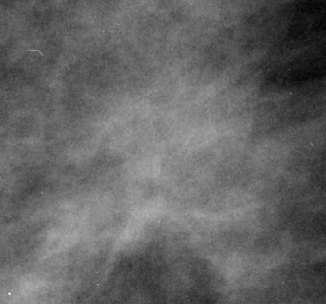
Region of interest cut from a scanned film mammogram (one marked finding); right breast; MLO view; BI-RADS breast density category 3 (scale 1–4).
- Marked abnormality: mass, shape architectural distortion, margins ill defined; BI-RADS assessment category 4; subtlety rating 2 on a 1 (subtle) to 5 (obvious) scale; pathology result (as recorded, not read from the image): malignant.